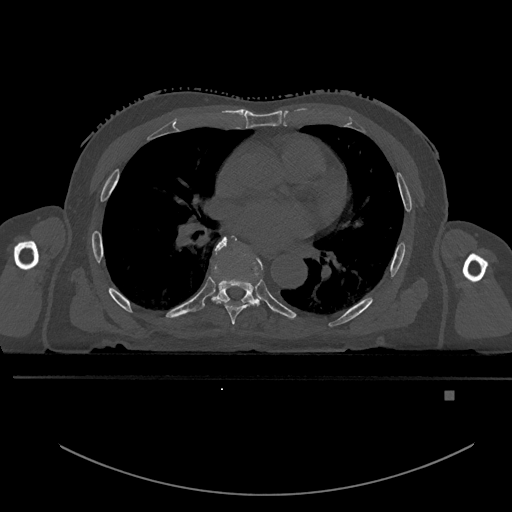
CT including the spine, one axial slice. Position 281 of 969 along the scan axis. Bone window (W 1800 / L 400 HU). 0.5 mm slice thickness. 512 × 512 image matrix, field of view 456 × 456 mm. Male patient, age 82 years. Case-level facts recorded for this patient, not image findings: primary cancer: prostate.
Annotated regions visible in this slice (semi-automatically segmented with operator editing):
- T6 vertebra: bounding box (x1, y1, x2, y2) in pixels: (211, 236, 259, 325)
- T7 vertebra: (213, 245, 261, 304)